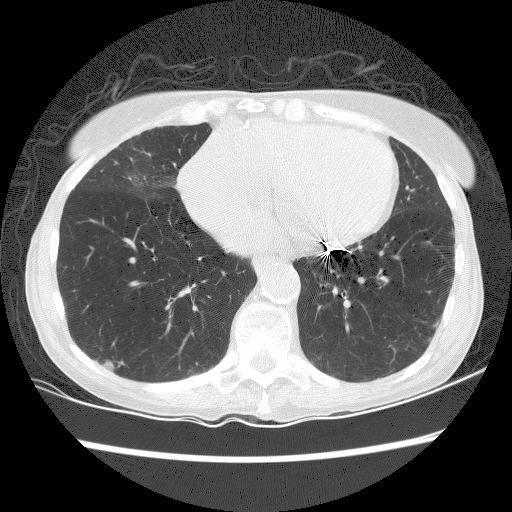
Low-dose screening chest CT, one axial slice. Slice 64 of 156 in the series (ordered by position). Reconstruction kernel BONE. 120 kVp. Lung window (W 1500 / L -600 HU). 2.5 mm slice thickness. 512 × 512 image matrix, field of view 320 × 320 mm.
Outlined on this slice (manually delineated by an expert):
- lesion 1 (tumor, lower lobe of right lung): bounding box (x1, y1, x2, y2) in pixels: (104, 360, 124, 370)